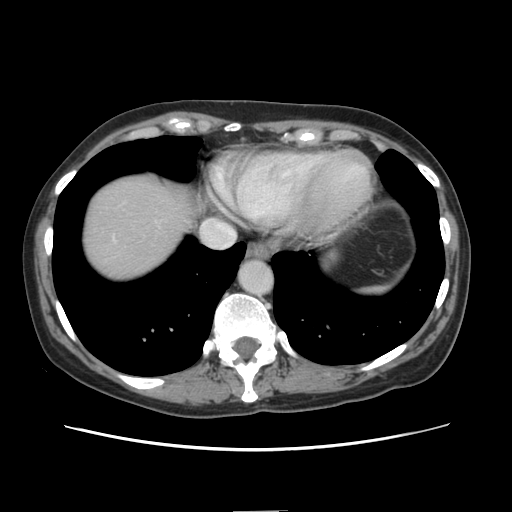
Contrast-enhanced abdominal CT, one axial slice. Slice 128 of 141 in the series (ordered by position). 120 kVp. Intravenous contrast given. Soft-tissue window (W 400 / L 40 HU). 2.5 mm slice thickness. 512 × 512 image matrix, field of view 350 × 350 mm. Female patient, age 63 years. Case-level facts recorded for this patient, not image findings: diagnosis: colorectal cancer liver metastases, imaged before liver resection.
Structures marked on this image (manually delineated by an expert):
- liver: bounding box [x1, y1, x2, y2] px = [81, 172, 192, 282]